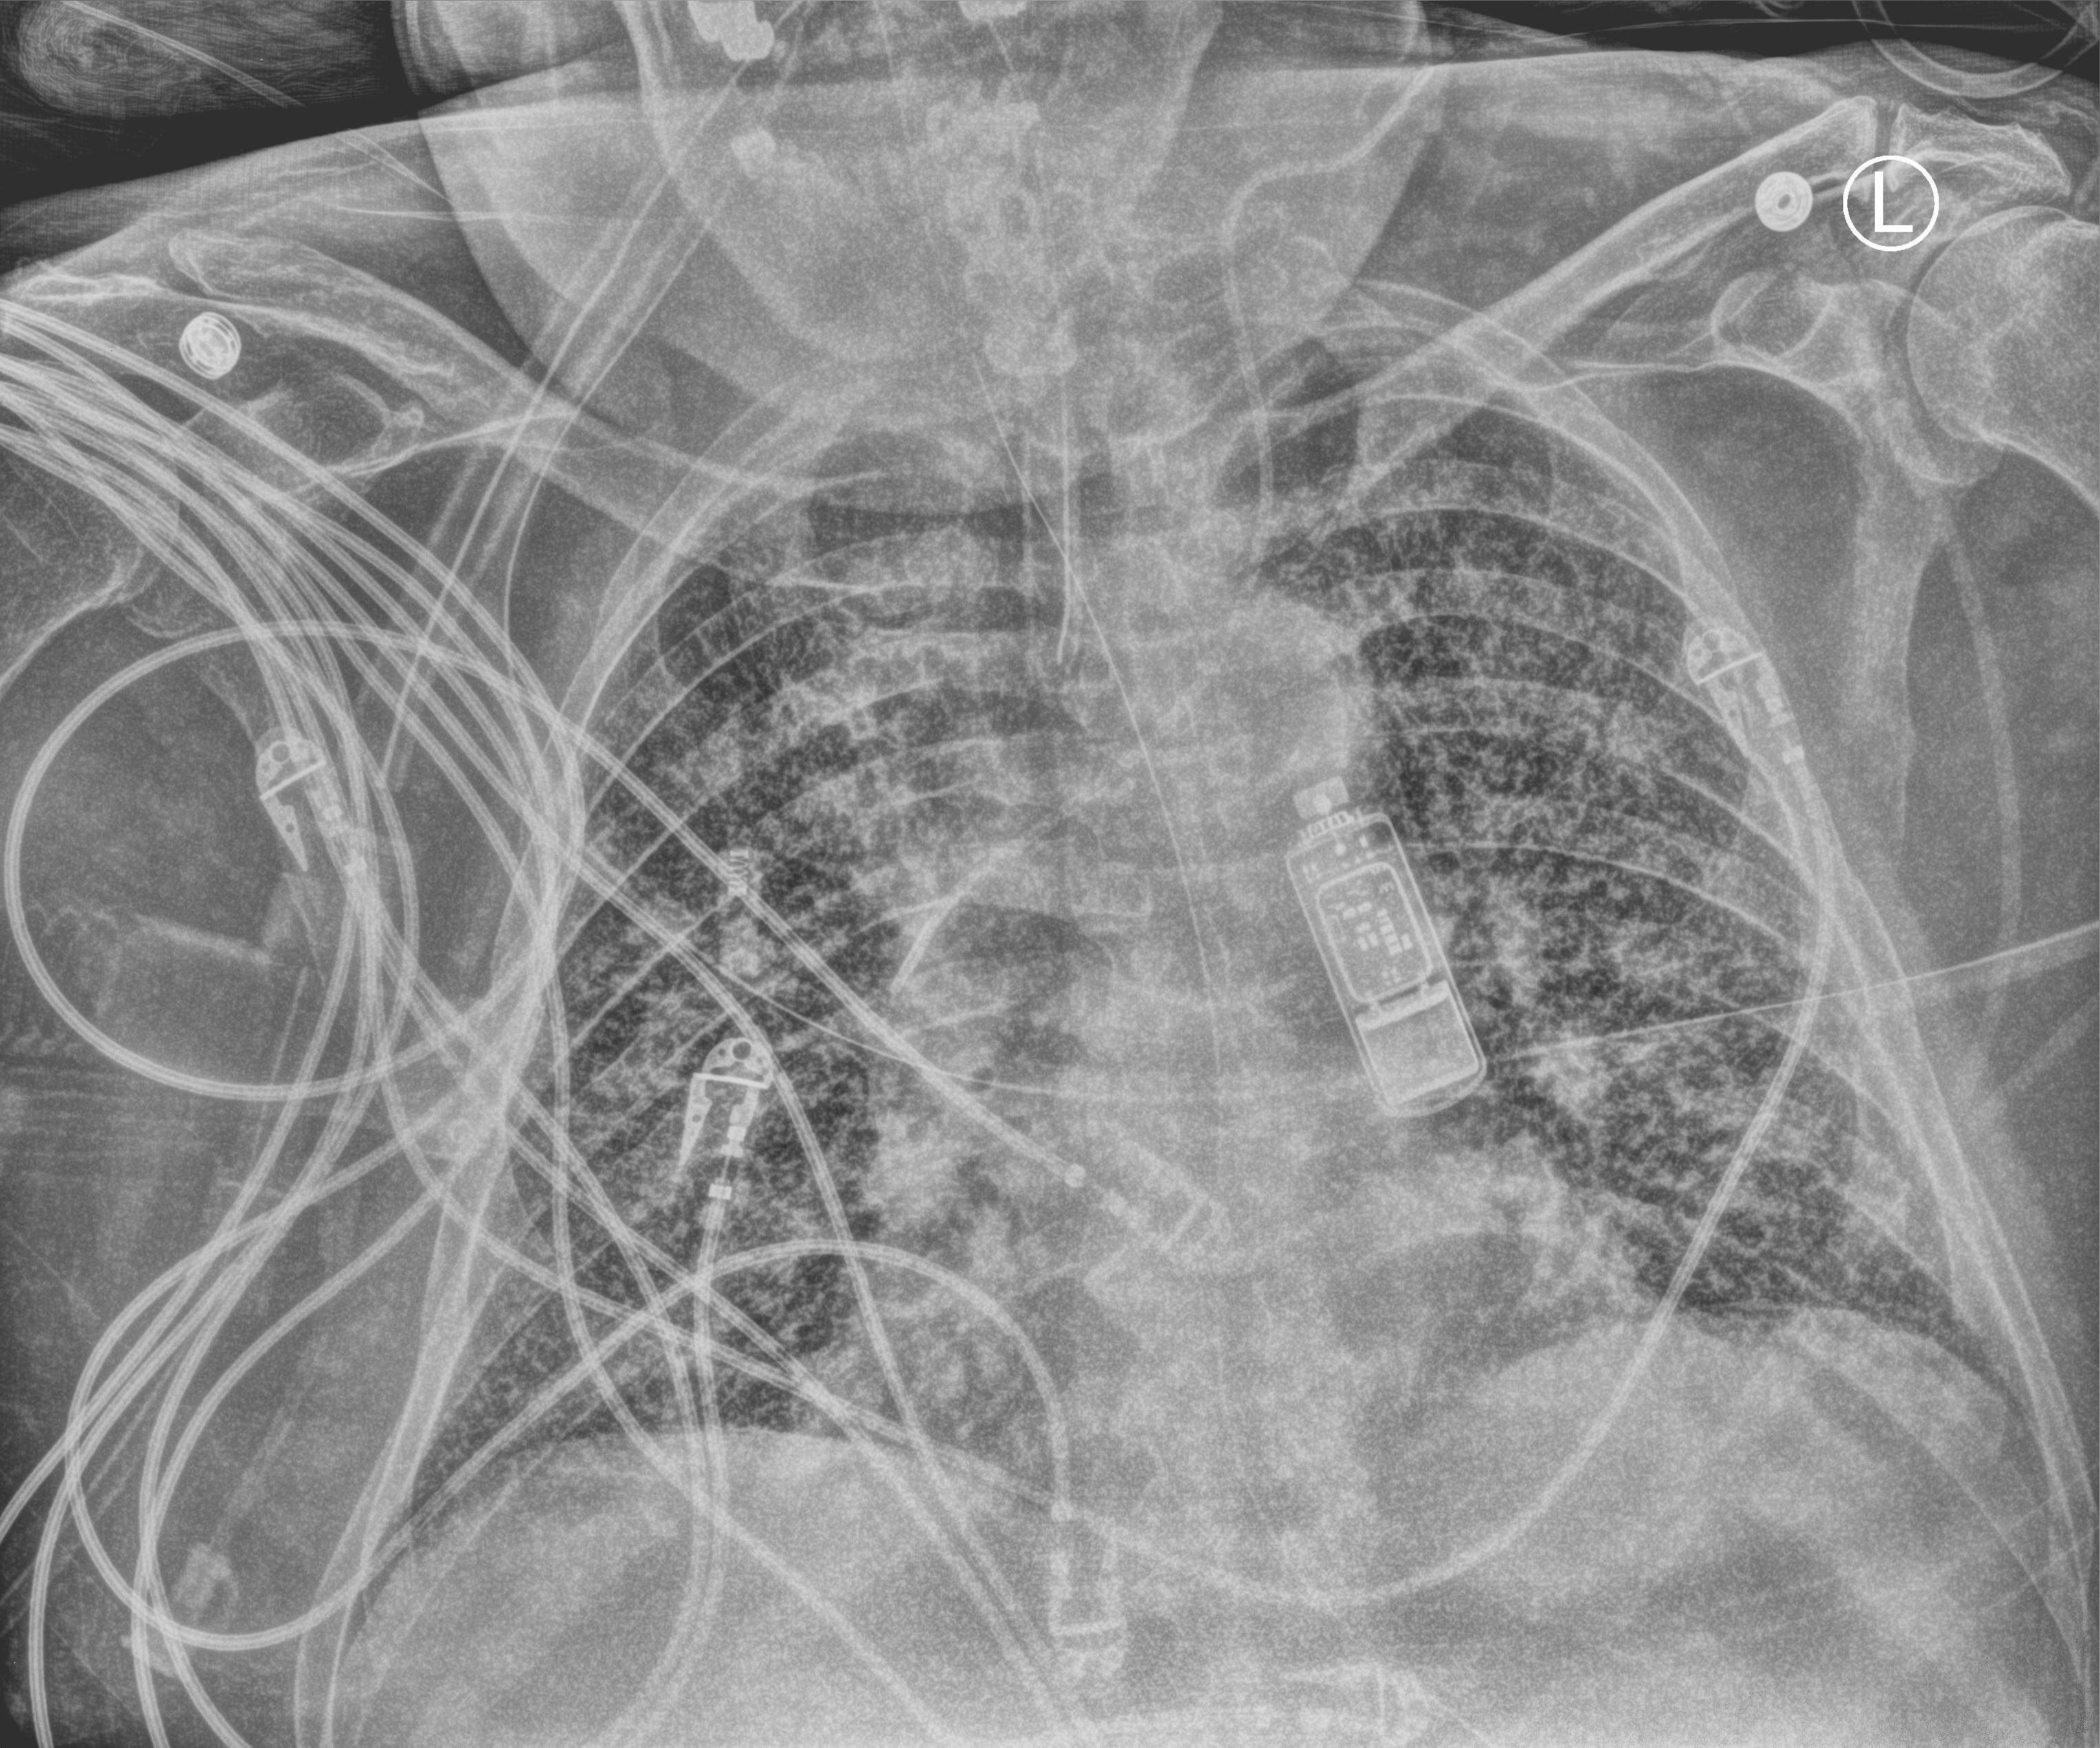
Bedside chest radiograph (computed radiography). Male patient hospitalised with COVID-19, age 60–74 years.
Admission-level facts for this patient (not findings on this image; timing relative to this image not recorded):
- admitted to intensive care during this hospital stay: yes
- length of hospital stay: 7 days
- mechanically ventilated during this hospital stay: yes